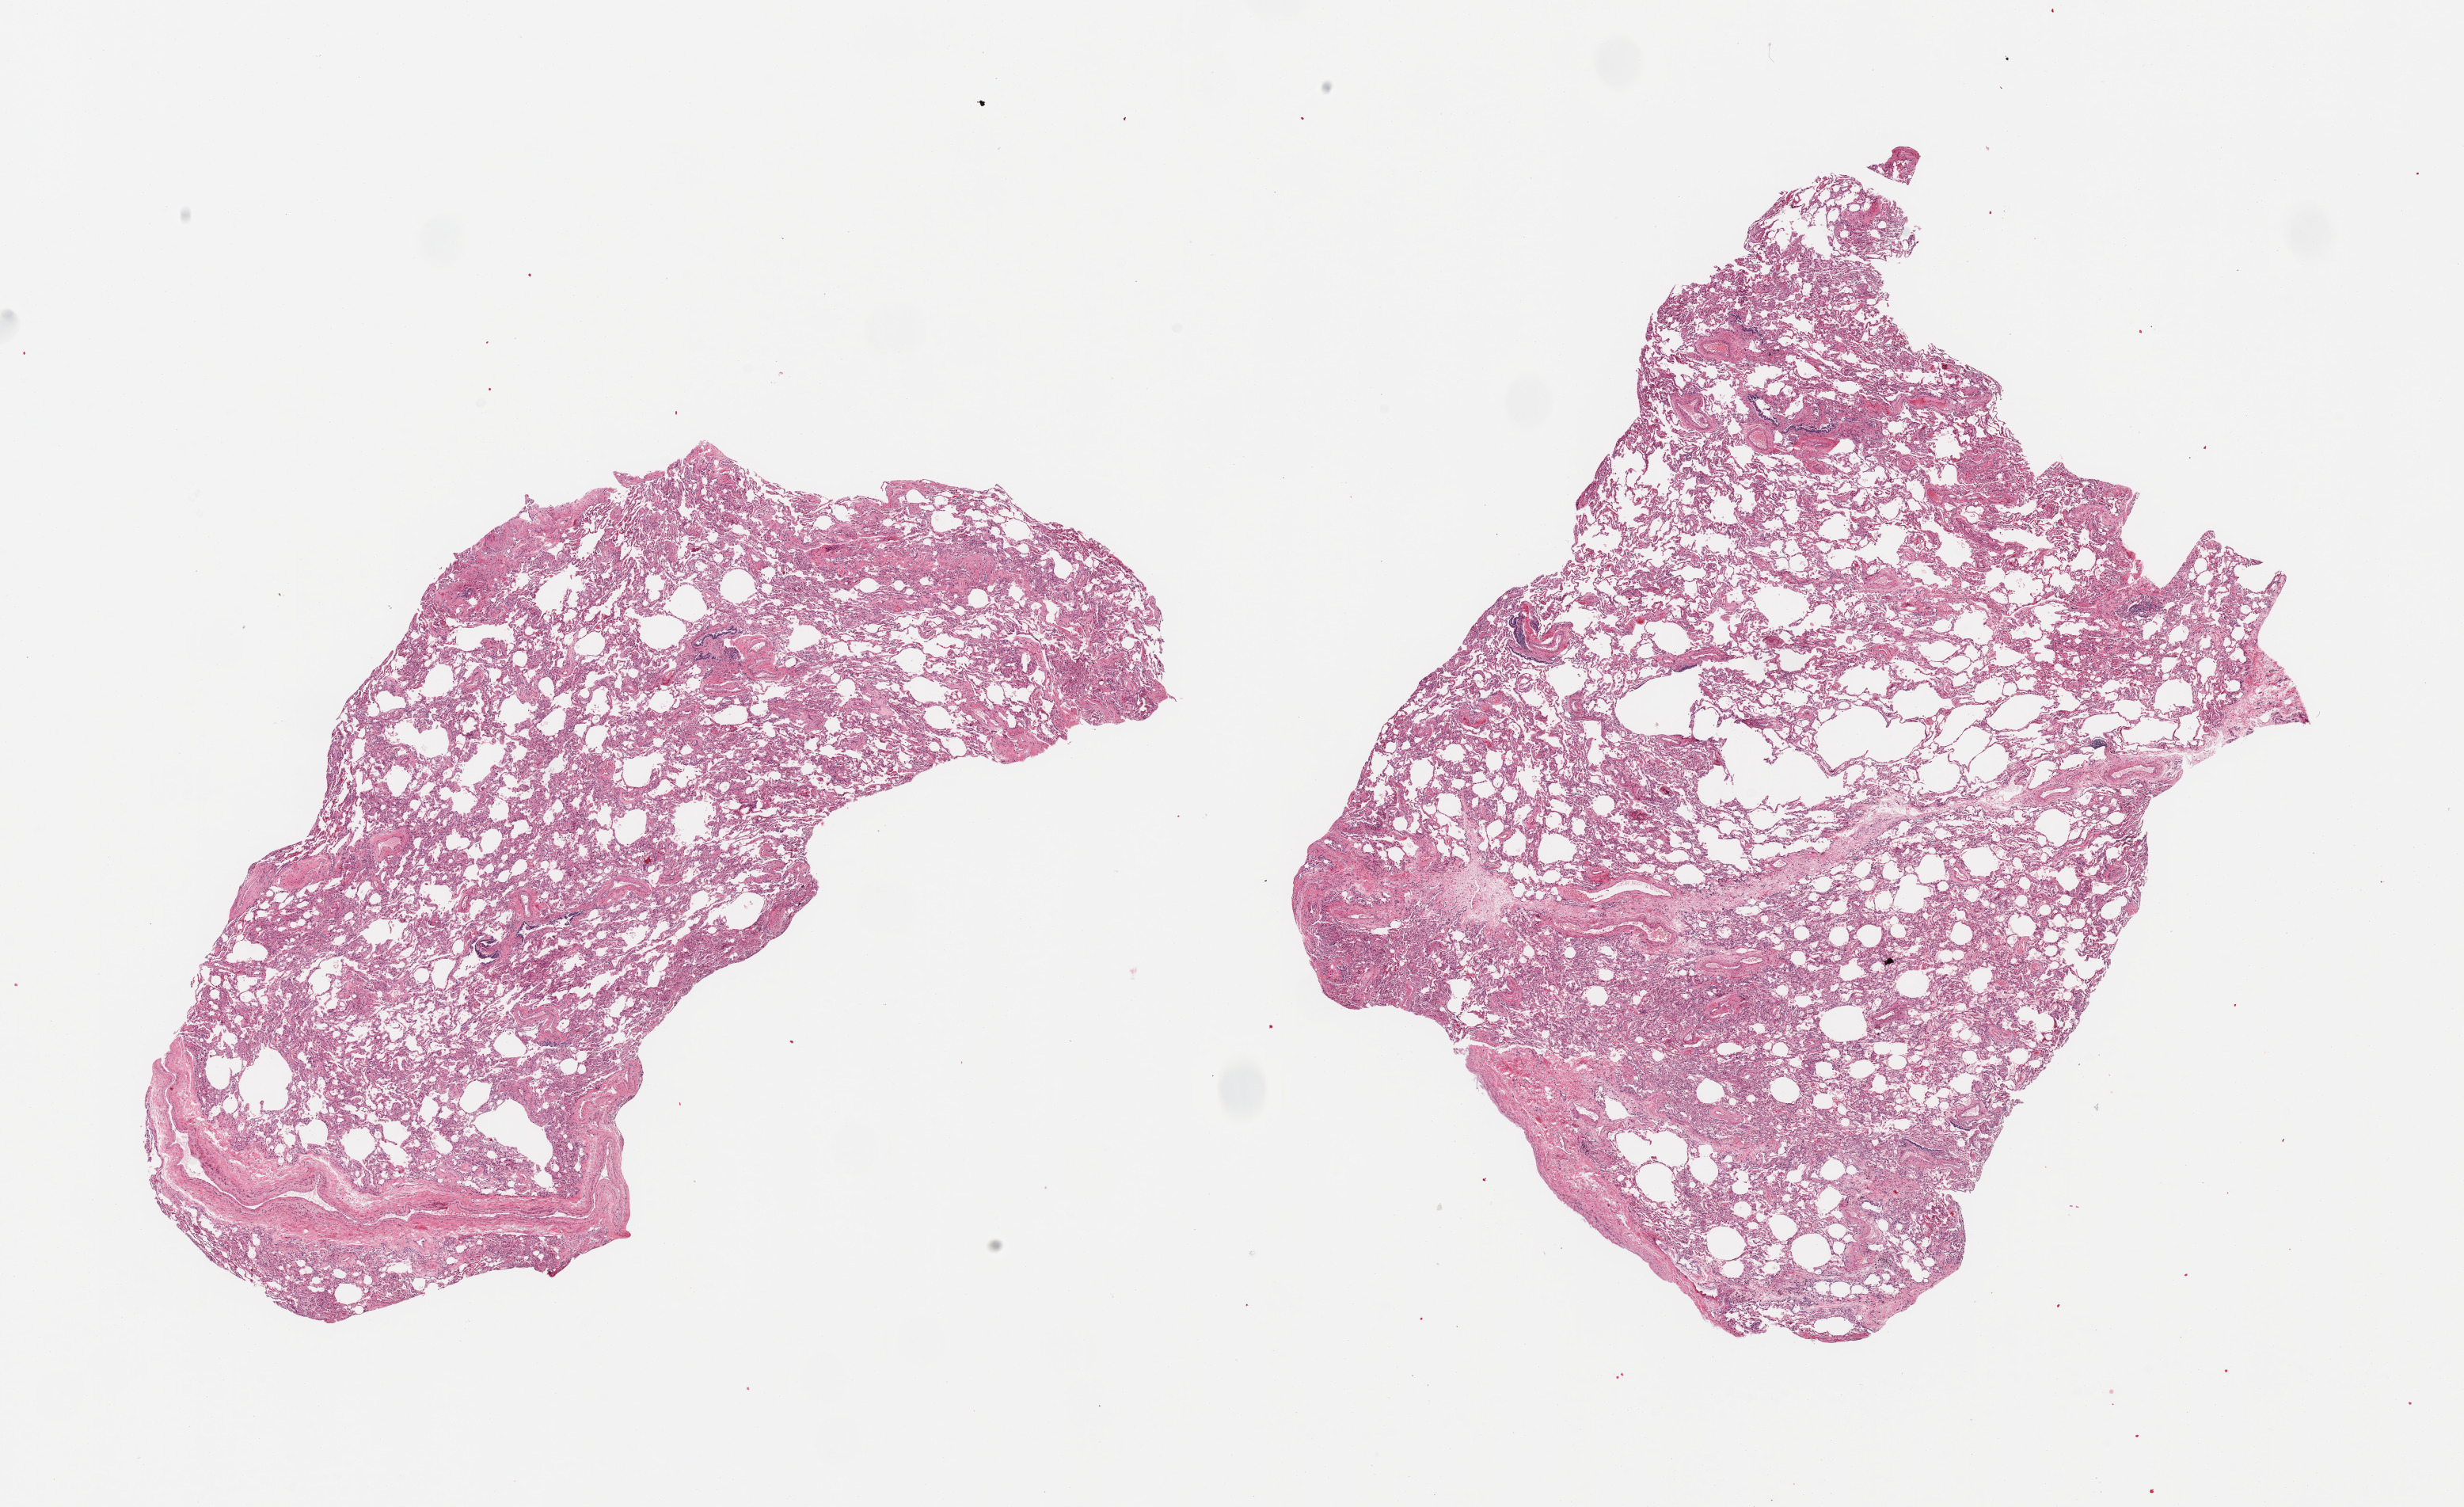
Digitized hematoxylin and eosin (H&E)-stained section, shown as a low-resolution overview of the whole scanned area (about 24.6 x 15.0 mm, slide scanned at 20x); PAXgene-fixed paraffin-embedded (PFPE) section; sampled site (target tissue): lung; donor tissue sample.
- review note (as recorded): 2 pieces; 1 piece includes large vessel, few thick walled vessels and focally collapsed alveolar spaces; congestion